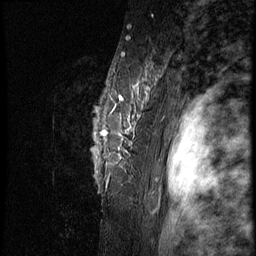
Breast MRI (dynamic contrast-enhanced), one sagittal slice. Position 62 of 66 along the scan axis. 3 images stored at this slice position (order not interpretable as contrast timing). 1.5 T. TE 4.2 ms, TR 8.9 ms. 2.5 mm slice thickness. 256 × 256 image matrix, field of view 200 × 200 mm. Female patient, age 39 years. Case-level facts recorded for this patient, not image findings: setting: breast cancer imaged before/during neoadjuvant chemotherapy; receptor status: HER2-positive.
Annotated regions visible in this slice (semi-automatically segmented with operator editing):
- analysis volume of interest (the breast-tissue region the enhancement analysis was run in; not a lesion): bounding box (x1, y1, x2, y2) in pixels: (52, 46, 166, 196)
- tumour enhancement mask (voxels above the 140 % enhancement threshold inside the analysis volume of interest): (104, 86, 140, 133)